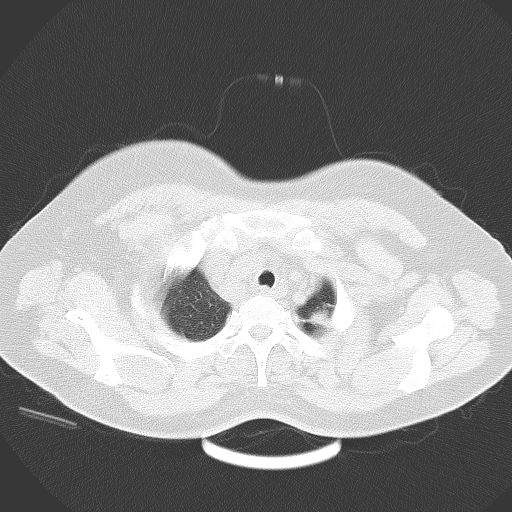
Chest CT, one axial slice; position 53 of 58 along the scan axis; 120 kVp; lung window (W 1500 / L -600 HU); 512 × 512 image matrix, field of view 390 × 390 mm. Patient: female, 53 years. From the clinical record (not read from this slice): clinical TNM (as recorded): T1c N3 M0.
Outlined on this slice (bounding box drawn by a radiologist):
- lung tumour (recorded histology: adenocarcinoma): bounding box <305,306,328,333> (left, top, right, bottom; pixels)